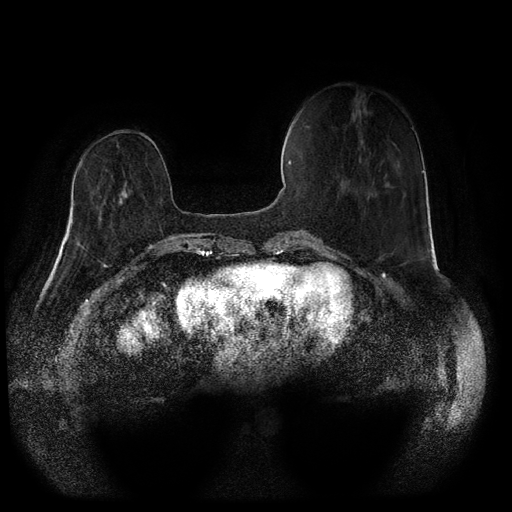
Breast MRI (dynamic contrast-enhanced, multi-phase), one axial slice; position 22 of 116 along the scan axis; dynamic contrast-enhanced series, time point 2 of 5 at this slice position (early post-contrast); 1.5 T; TE 2.6 ms, TR 5.3 ms; 2 mm slice thickness; 512 × 512 image matrix, field of view 360 × 360 mm. Female patient, age 71 years.
Outlined on this slice (semi-automatically segmented with operator editing):
- breast lesion (labelled 'tumour' in the annotation; benign lesions carry a separate 'benign' label): box from (x=117, y=189) to (x=127, y=204) px